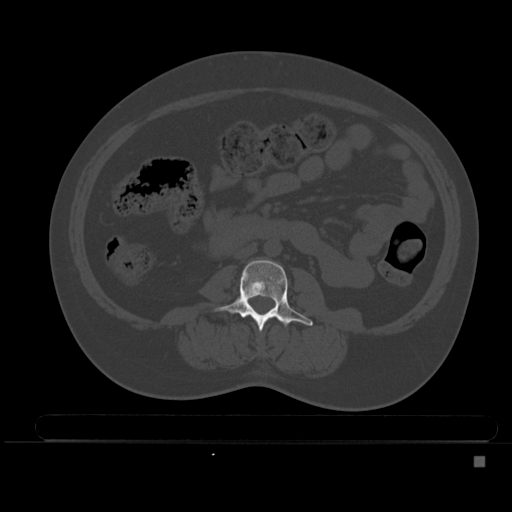
CT including the spine, one axial slice; position 152 of 495 along the scan axis; bone window (W 1800 / L 400 HU); 1.5 mm slice thickness; 512 × 512 image matrix, field of view 404 × 404 mm. Patient: female, 33 years. Case-level facts recorded for this patient, not image findings: primary cancer: breast.
Outlined on this slice (semi-automatically segmented with operator editing):
- L3 vertebra: bounding box [x1, y1, x2, y2] px = [212, 260, 313, 331]